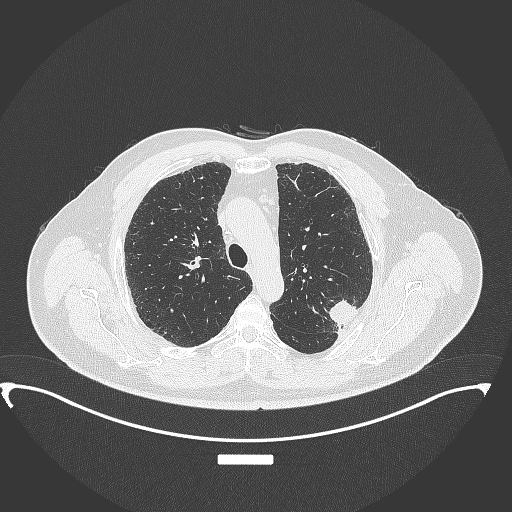
Chest CT, one axial slice. Position 264 of 350 along the scan axis. Reconstruction kernel B70f. Lung window (W 1500 / L -600 HU). 1 mm slice thickness. 512 × 512 image matrix, field of view 459 × 459 mm. Male patient, age 64 years. From the clinical record (not read from this slice): clinical TNM (as recorded): T1c N1 M1.
Structures marked on this image (rectangle marked by the reading radiologist):
- lung tumour (recorded histology: adenocarcinoma): box from (x=326, y=295) to (x=364, y=328) px